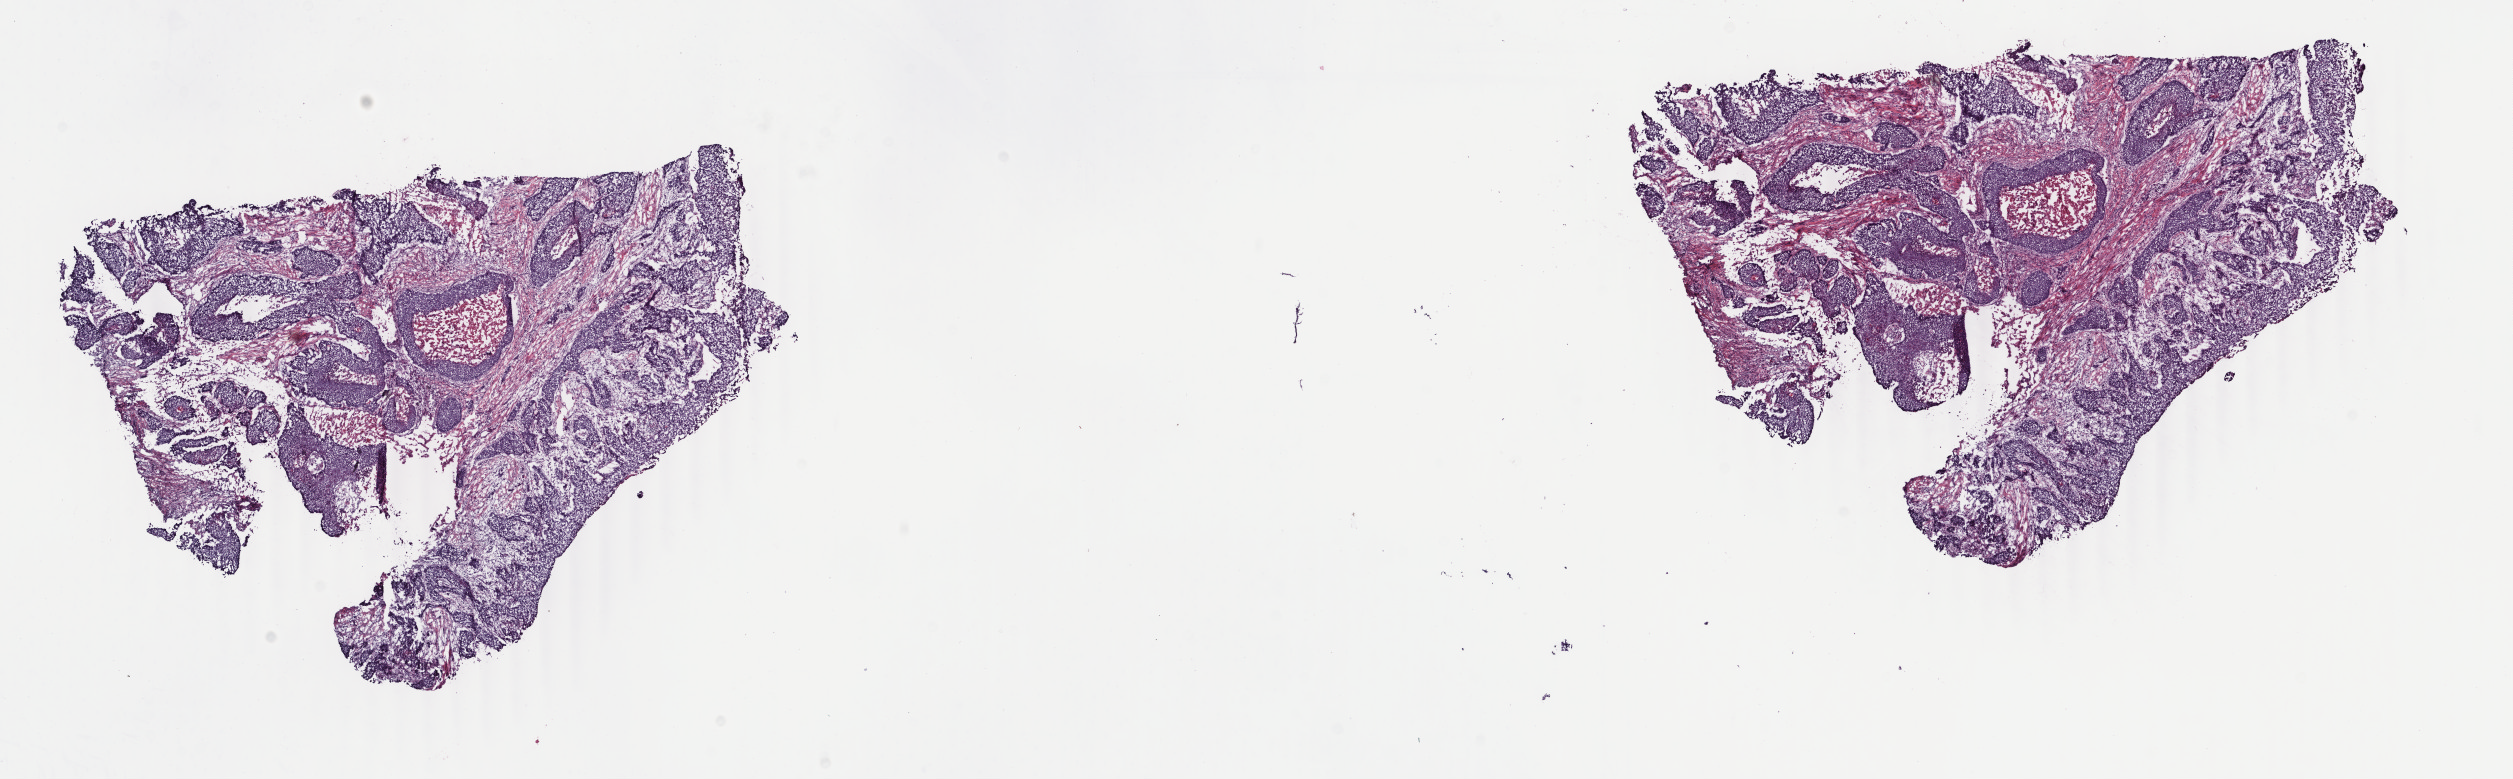
Digitized Hematoxylin and eosin (H&E) stained tissue section (whole slide) — whole scanned area (about 20.0 x 6.2 mm, acquisition: 40x scan) shown as a low-resolution overview; frozen section; head and neck, primary tumour sample. Male, age 73 years at initial diagnosis. Histologic grade: G3 (poorly differentiated). Composition of this section per pathologist review: tumour cells 40%, tumour nuclei 75%, normal cells 0%, stromal cells 50%, necrosis 10%. Infiltration values recorded for this section: lymphocyte infiltration 4%, monocyte infiltration 1%, neutrophil infiltration 1%.
Lymph nodes positive (case pathology): 1 of 49 examined. Diagnosis: Basaloid squamous cell carcinoma (cheek mucosa). TNM: T2 N1 M0. AJCC pathologic stage: III (7th edition).